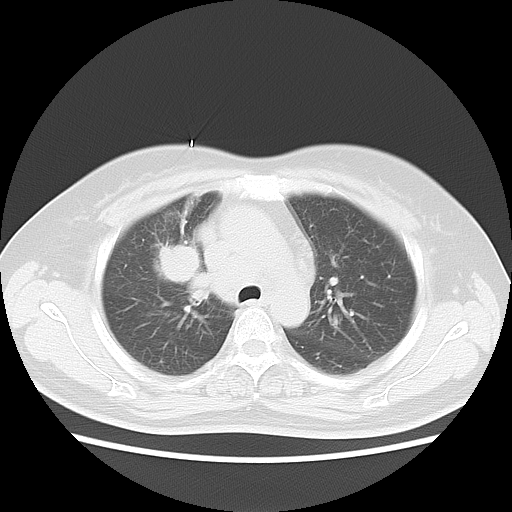
Chest CT, one axial slice; position 10 of 18 along the scan axis; reconstruction kernel LUNG; 120 kVp; lung window (W 1500 / L -600 HU); 5 mm slice thickness; 512 × 512 image matrix, field of view 350 × 350 mm. Patient: female, 54 years. From the clinical record (not read from this slice): clinical TNM (as recorded): T2 N3 M0; histopathological grade: G3.
Structures marked on this image (bounding box drawn by a radiologist):
- lung tumour (recorded histology: small cell carcinoma): box from (x=146, y=237) to (x=200, y=288) px